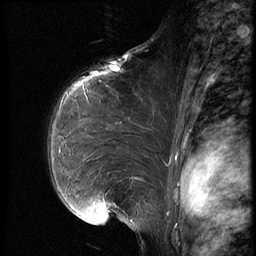
Breast MRI (dynamic contrast-enhanced), one sagittal slice. Position 47 of 66 along the scan axis. Dynamic contrast-enhanced series, image 2 of 3 at this slice position (ordered by acquisition). 1.5 T. TE 4.2 ms, TR 8.9 ms. 256 × 256 image matrix. Female patient, age 39 years. From the clinical record (not read from this slice): setting: breast cancer imaged before/during neoadjuvant chemotherapy; receptor status: HER2-positive.
Outlined on this slice (semi-automatically segmented with operator editing):
- analysis volume of interest (the breast-tissue region the enhancement analysis was run in; not a lesion): bounding box <43,75,171,218> (left, top, right, bottom; pixels)
- tumour enhancement mask (voxels above the 140 % enhancement threshold inside the analysis volume of interest): <89,87,168,216>